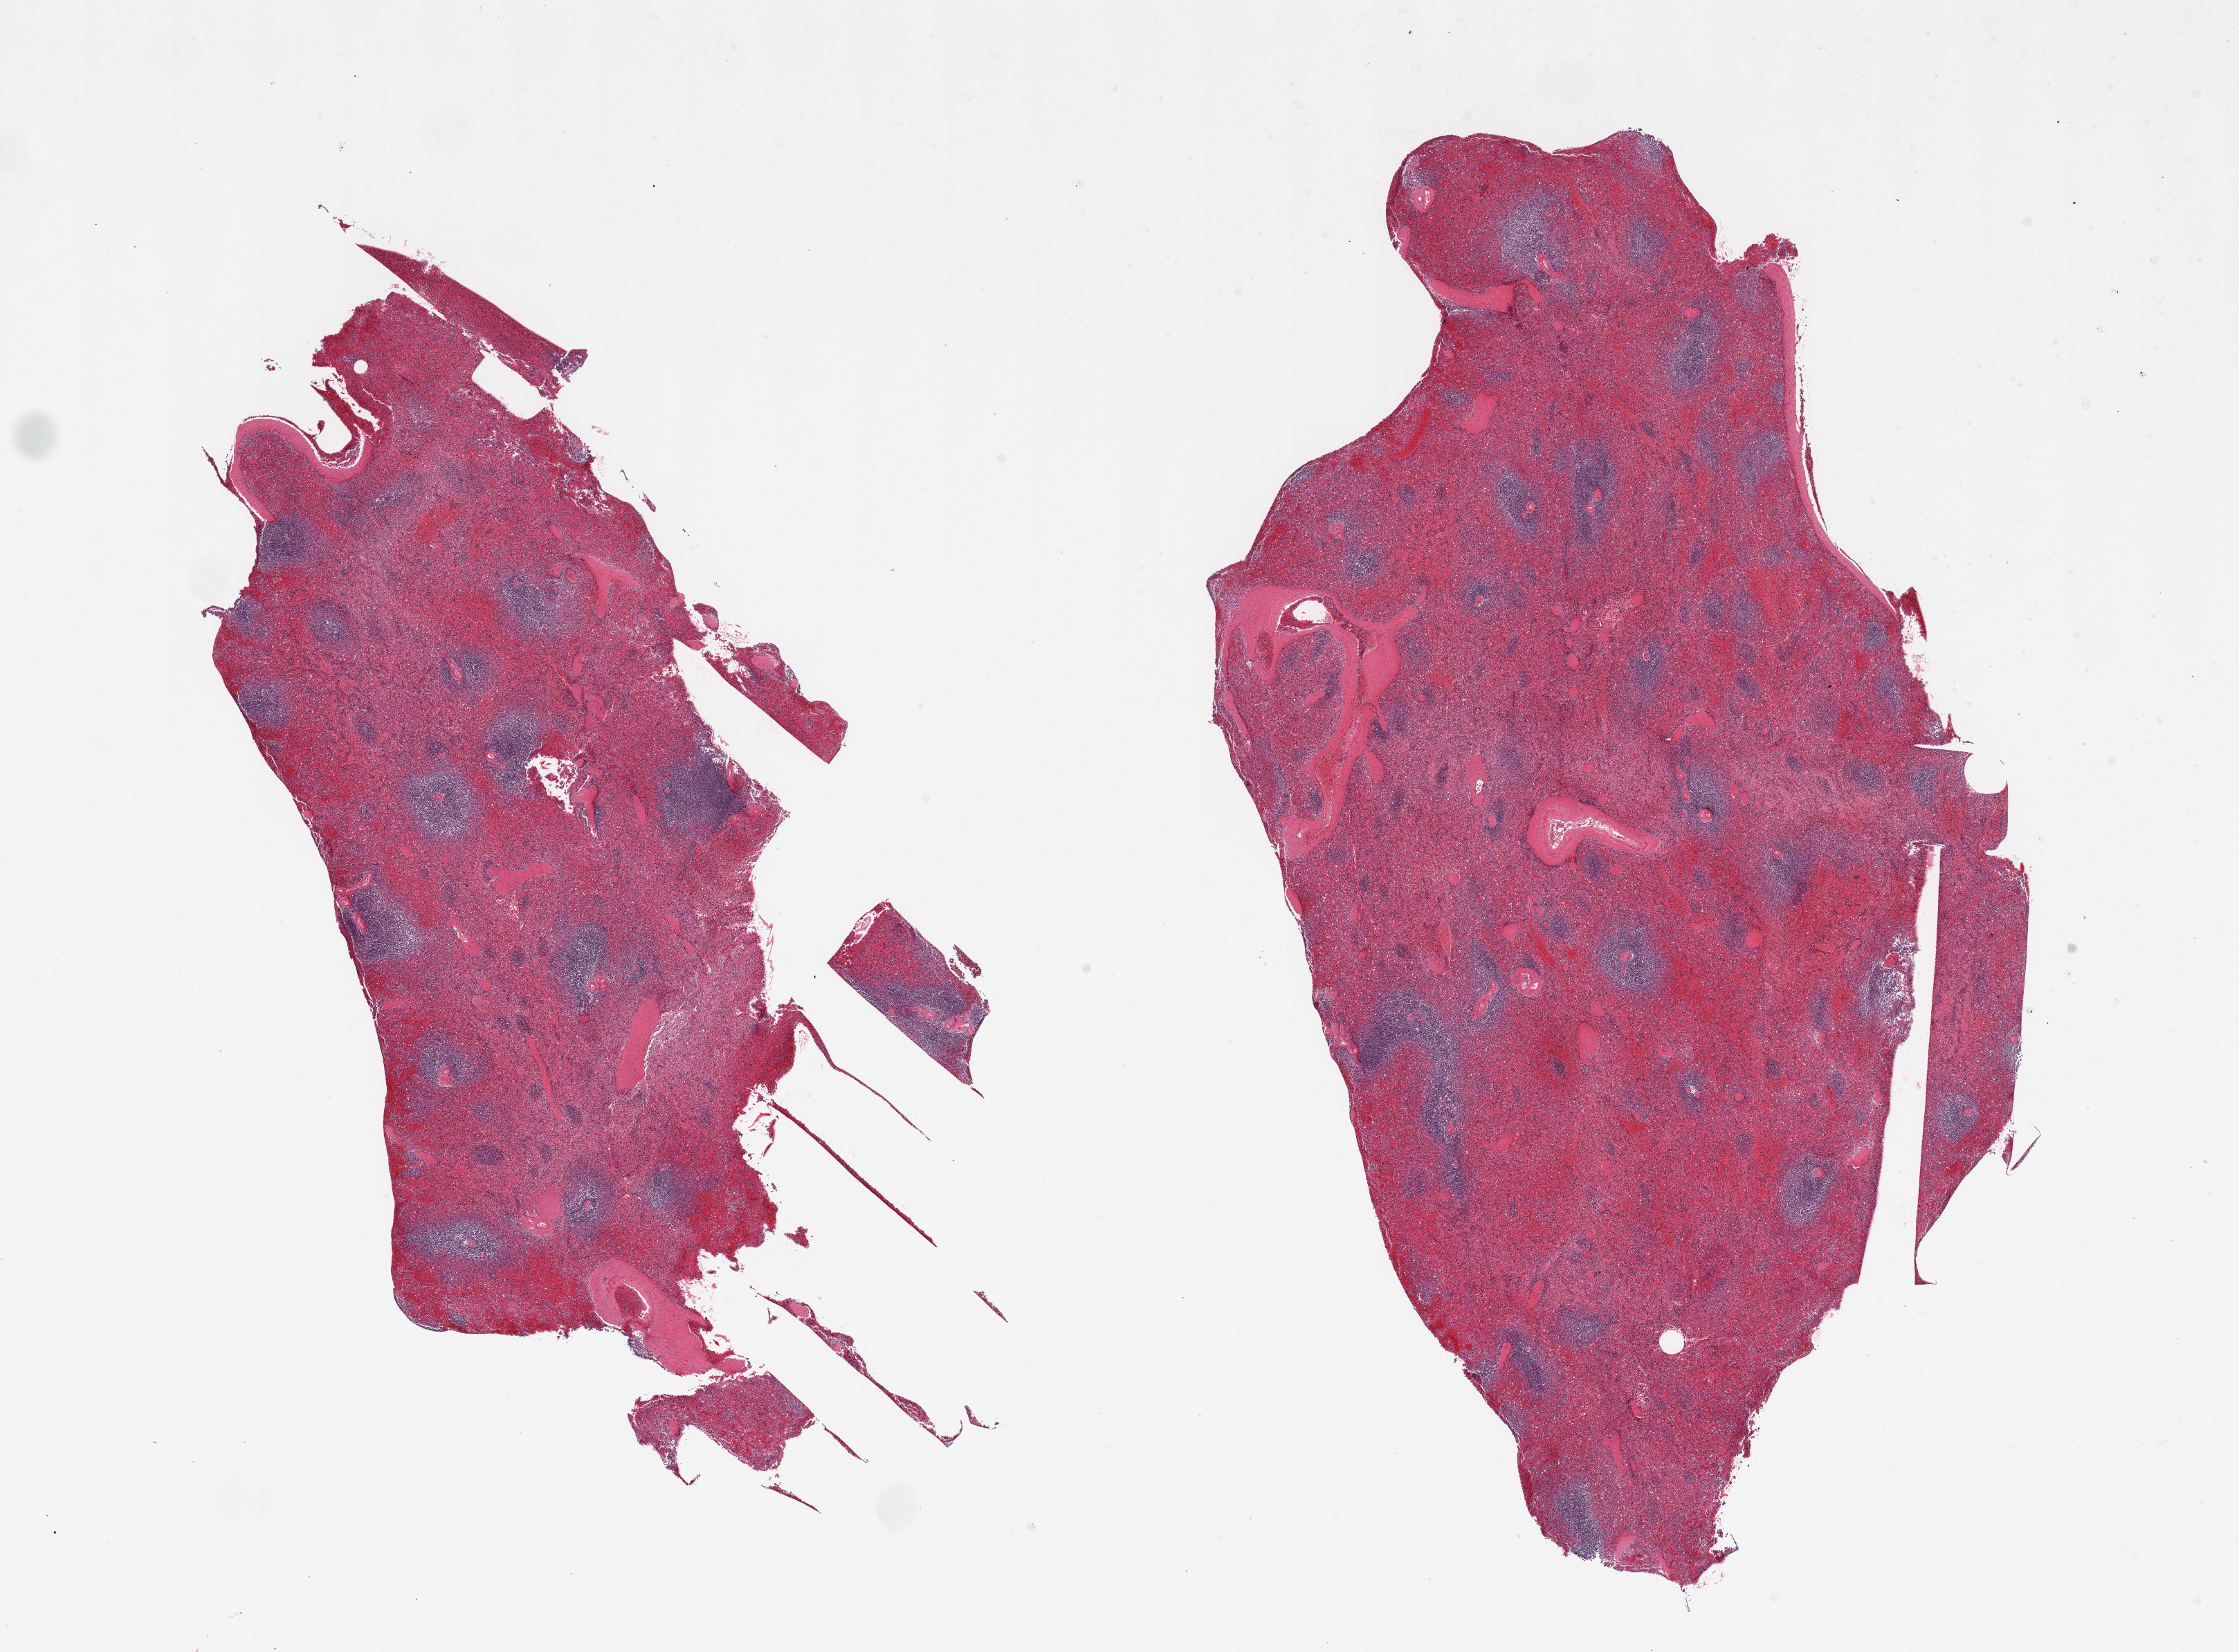
H&E whole-slide image — shown as a low-resolution overview of the whole scanned area (about 25.6 x 18.9 mm), PAXgene-fixed, paraffin-embedded tissue, target tissue: spleen, donor tissue sample. Donor sex: female.
Reviewer comment on this tissue sample: 2 pieces; congestion.